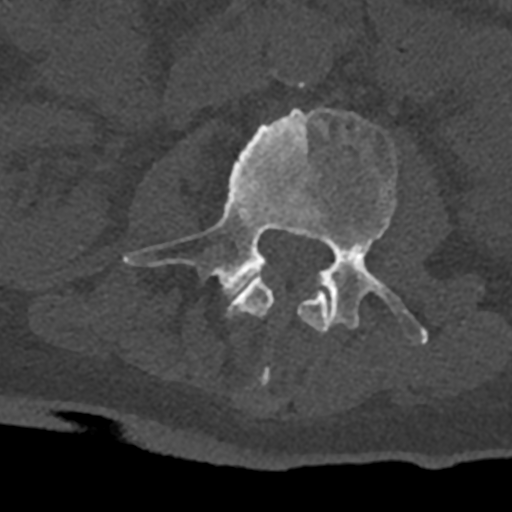
CT including the spine, one axial slice. Position 335 of 797 along the scan axis. 120 kVp. Bone window (W 1800 / L 400 HU). 0.5 mm slice thickness. 512 × 512 image matrix, field of view 160 × 160 mm. Male patient, age 74 years. From the clinical record (not read from this slice): primary cancer: renal; vertebrae with lytic lesions (as recorded): T10, L1, L2, L3, L4, L5.
Annotated regions visible in this slice (semi-automatically segmented with operator editing):
- L2 vertebra: bounding box [x1, y1, x2, y2] px = [226, 277, 330, 388]
- L3 vertebra: [123, 106, 428, 344]